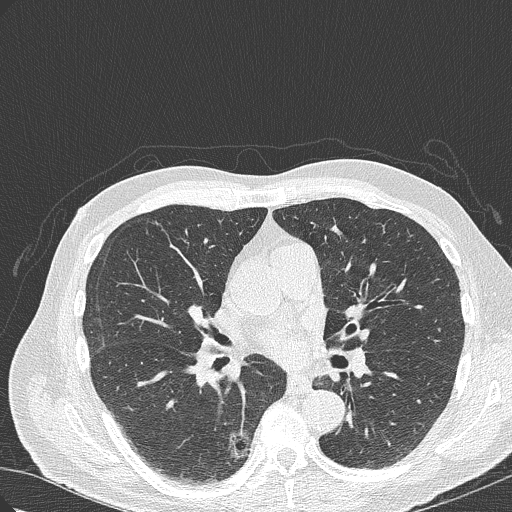
Axial slice from a low-dose chest CT screening exam, baseline screening round, lung window (W 1500 / L -600 HU), 1 mm slice thickness, lung (sharp) reconstruction kernel (B50f), slice 148 of 322 in the series. Male participant, aged 70 years at enrolment. Current smoker at enrolment.
Expert reader's lesion annotation, box from (x=198, y=420) to (x=261, y=481) px. The screening reader recorded 4 non-calcified nodules or masses ≥4 mm on this exam (right lower lobe, right lower lobe, right upper lobe, right lower lobe); which of them this box marks is not recorded. Official screen result: positive, change unspecified: nodule(s) >= 4 mm or enlarging nodule(s), mass(es), or other non-specific abnormalities suspicious for lung cancer. Lung cancer was diagnosed 978 days after this screen: bronchiolo-alveolar adenocarcinoma, NOS, right lower lobe, poorly differentiated (G3), stage IB (AJCC 6th edition), 30 mm at pathology.